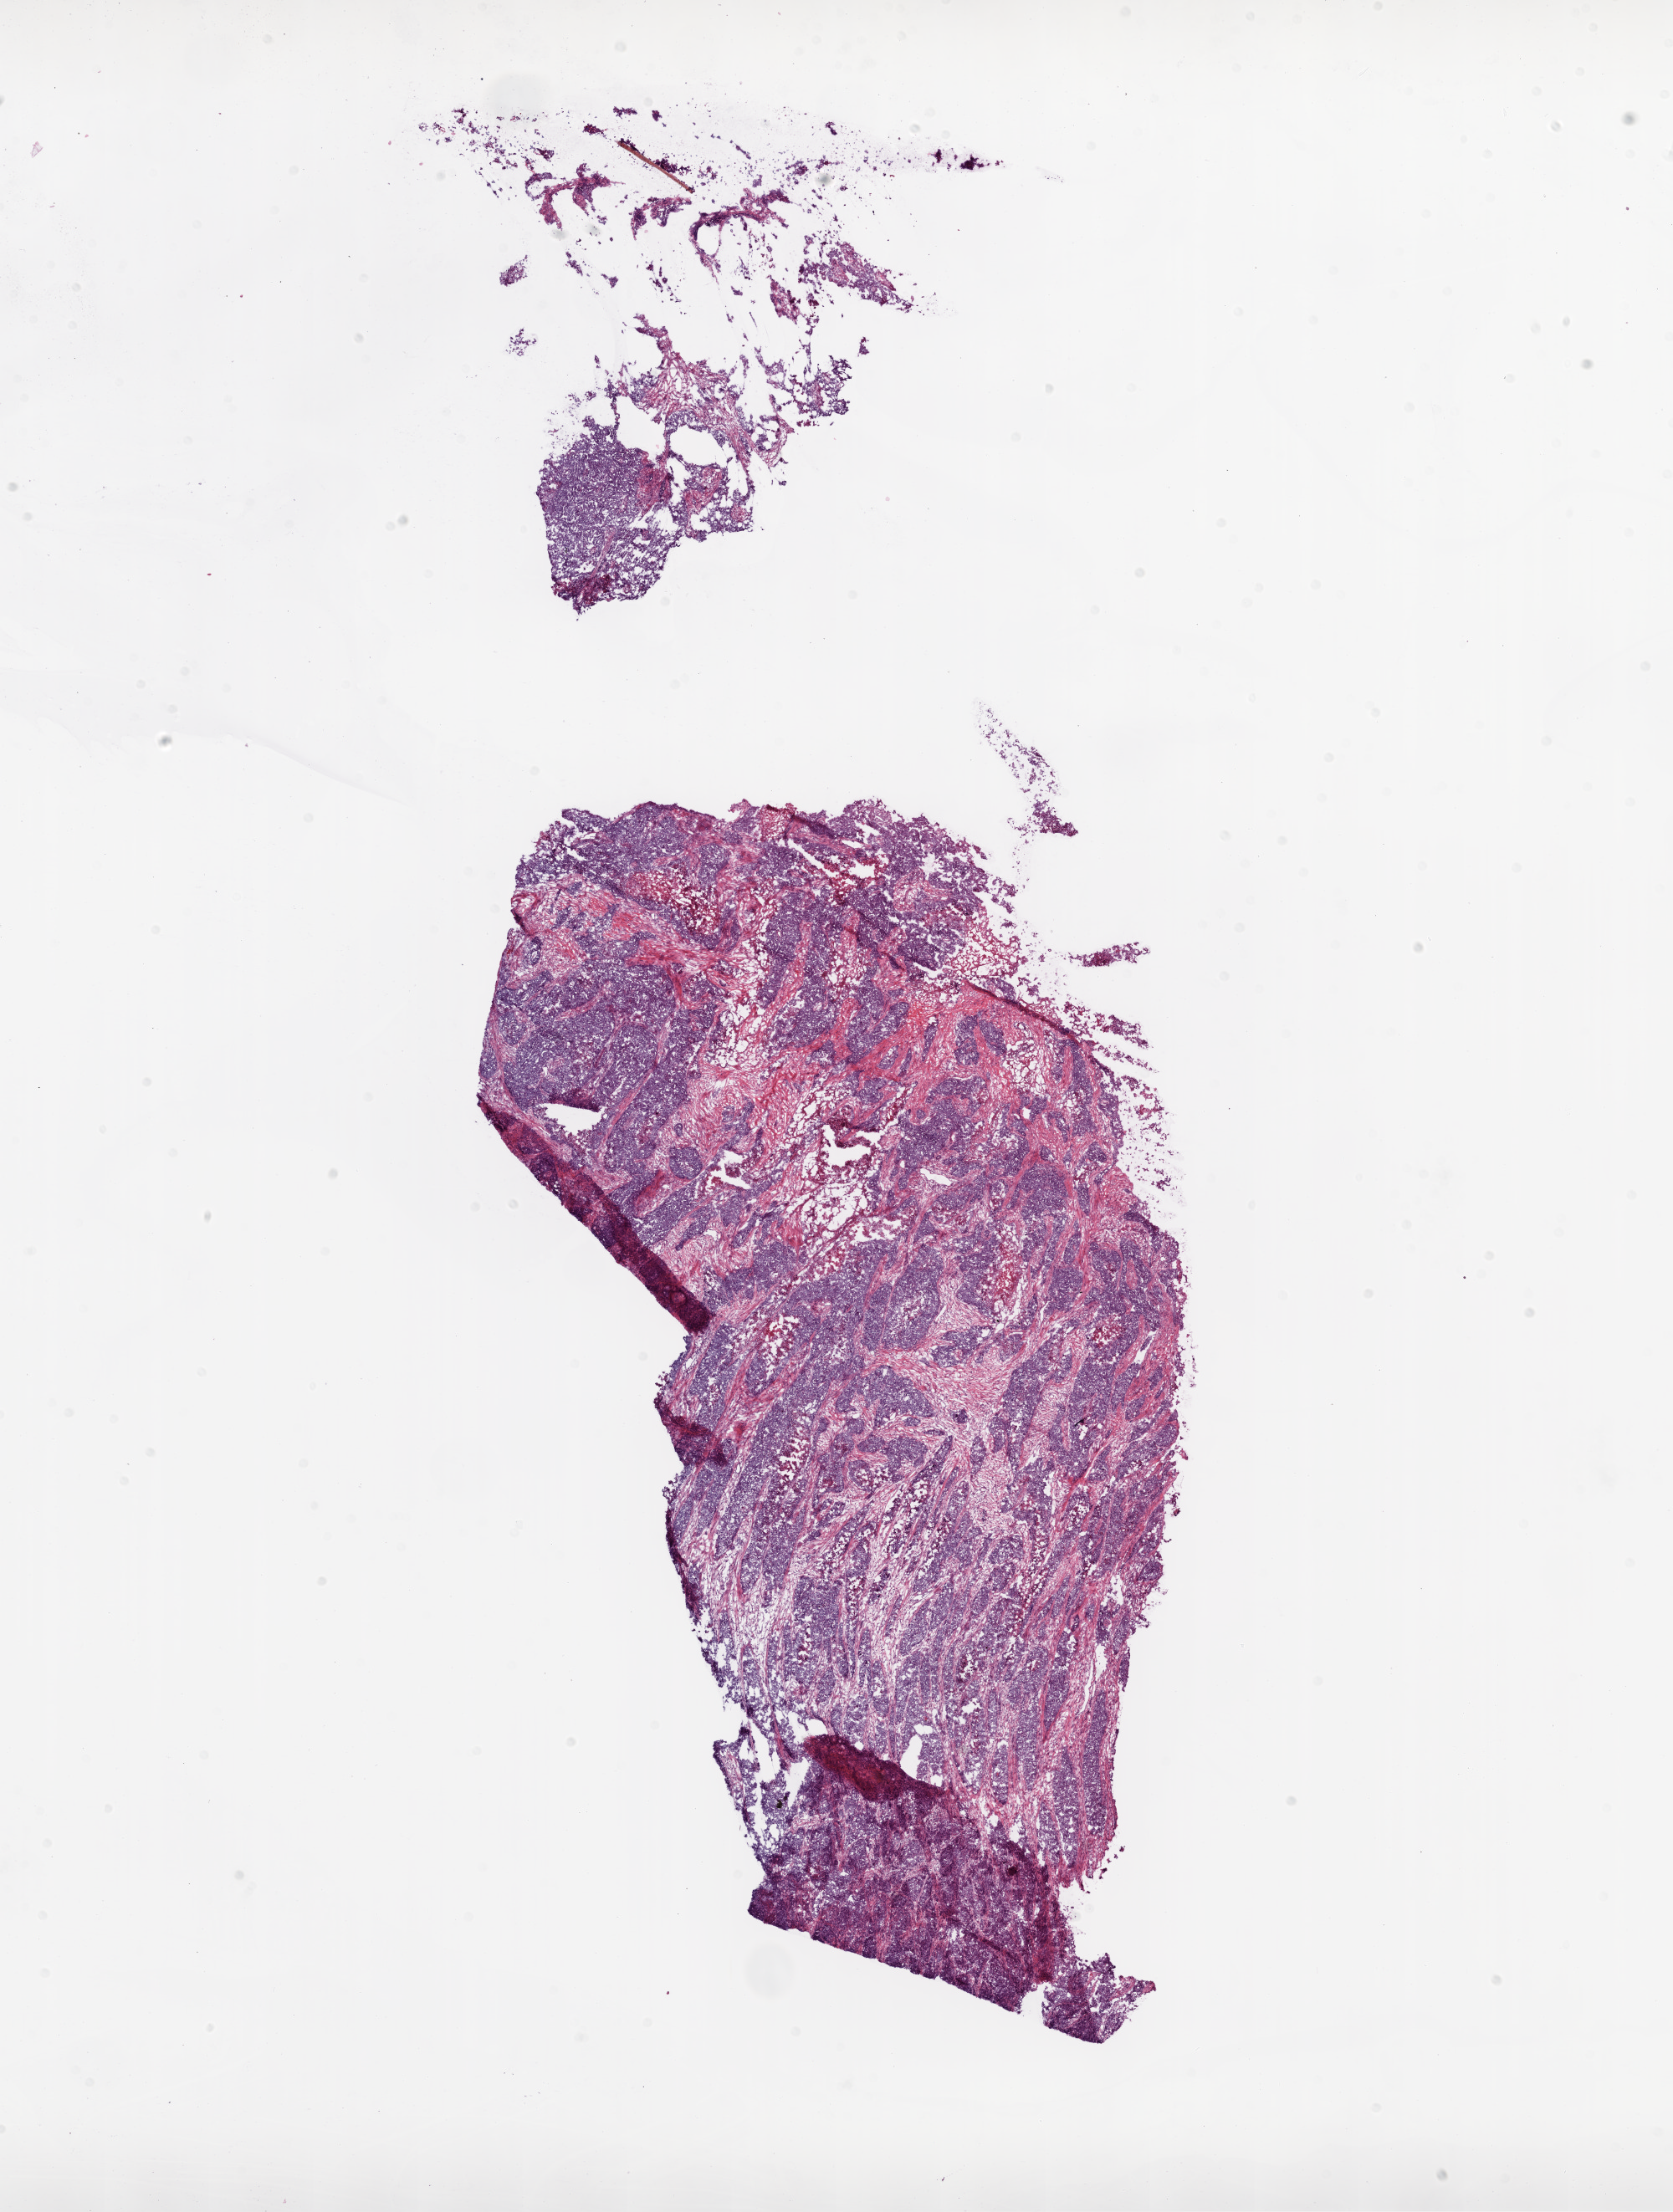
H&E whole-slide image — a low-resolution overview of the entire scanned area, about 16.0 x 21.2 mm (from a 20x scan), frozen section from the bottom of the tissue portion, ovary, primary tumour sample. Female, age 49 years at initial diagnosis.
Pathologic diagnosis: Serous cystadenocarcinoma, NOS.